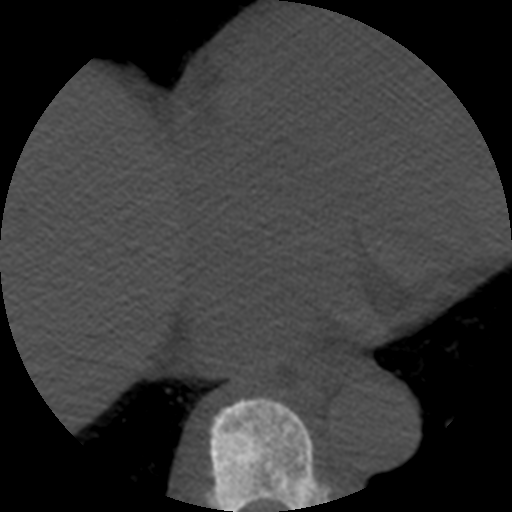
CT including the spine, one axial slice; slice 309 of 508 in the series (ordered by position); reconstruction kernel STANDARD; bone window (W 1800 / L 400 HU); 1.25 mm slice thickness; 512 × 512 image matrix, field of view 160 × 160 mm. Patient age 57 years. From the clinical record (not read from this slice): primary cancer: prostate.
Annotated regions visible in this slice (semi-automatic segmentation, software-assisted and operator-edited):
- T8 vertebra: bounding box <205,397,330,512> (left, top, right, bottom; pixels)